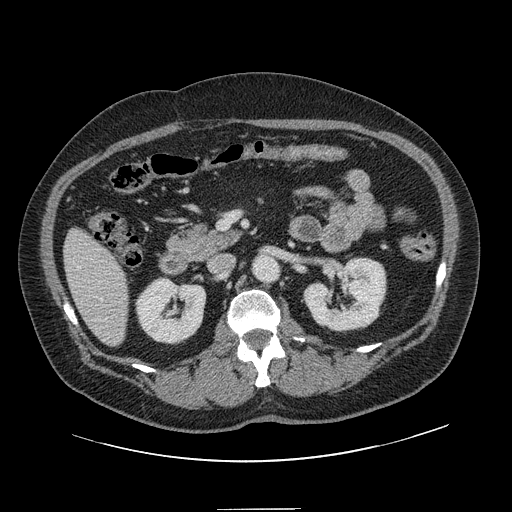
Contrast-enhanced abdominal CT, one axial slice. Position 53 of 154 along the scan axis. Intravenous contrast given. Soft-tissue window (W 400 / L 40 HU). 512 × 512 image matrix, field of view 451 × 451 mm. Male patient, age 61 years. From the clinical record (not read from this slice): diagnosis: colorectal cancer liver metastases, imaged before liver resection; multiple liver metastases: yes; largest metastasis: 2.6 cm; disease in both lobes: yes.
Structures marked on this image (outlined manually by an expert reader):
- hepatic veins: bounding box (x1, y1, x2, y2) in pixels: (78, 266, 103, 301)
- liver: (65, 230, 128, 346)
- planned liver remnant (the part of the liver to remain after resection): (65, 230, 128, 346)